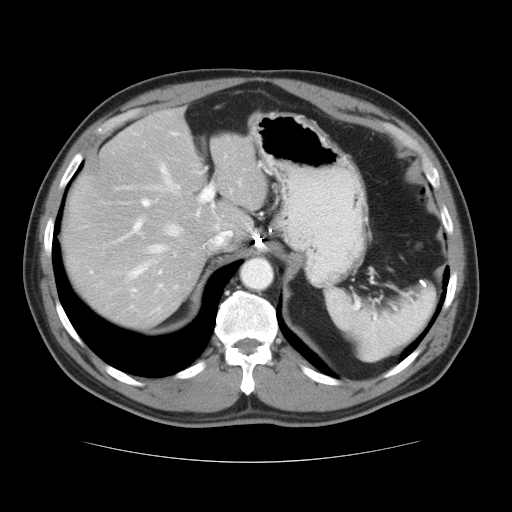
Contrast-enhanced abdominal CT, one axial slice; reconstruction kernel STANDARD; 120 kVp; intravenous contrast given; soft-tissue window (W 400 / L 40 HU); 5 mm slice thickness; 512 × 512 image matrix, field of view 374 × 374 mm. Male patient, age 66 years. Case-level facts recorded for this patient, not image findings: diagnosis: colorectal cancer liver metastases, imaged before liver resection.
Structures marked on this image (outlined manually by an expert reader):
- hepatic veins: bounding box <116,163,233,278> (left, top, right, bottom; pixels)
- liver: <62,107,268,329>
- planned liver remnant (the part of the liver to remain after resection): <62,134,268,329>
- portal vein (with intrahepatic branches): <116,184,215,242>